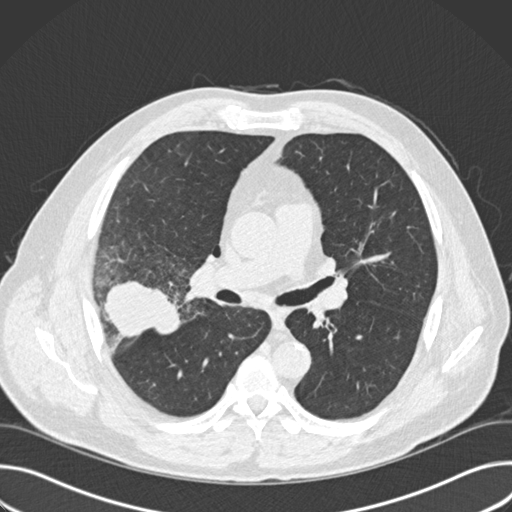
Low-dose screening chest CT, one axial slice. 120 kVp. Lung window (W 1500 / L -600 HU). 2 mm slice thickness. 512 × 512 image matrix.
Outlined on this slice (manually delineated by an expert):
- lesion 1 (tumor, upper lobe of right lung): box from (x=103, y=281) to (x=182, y=338) px